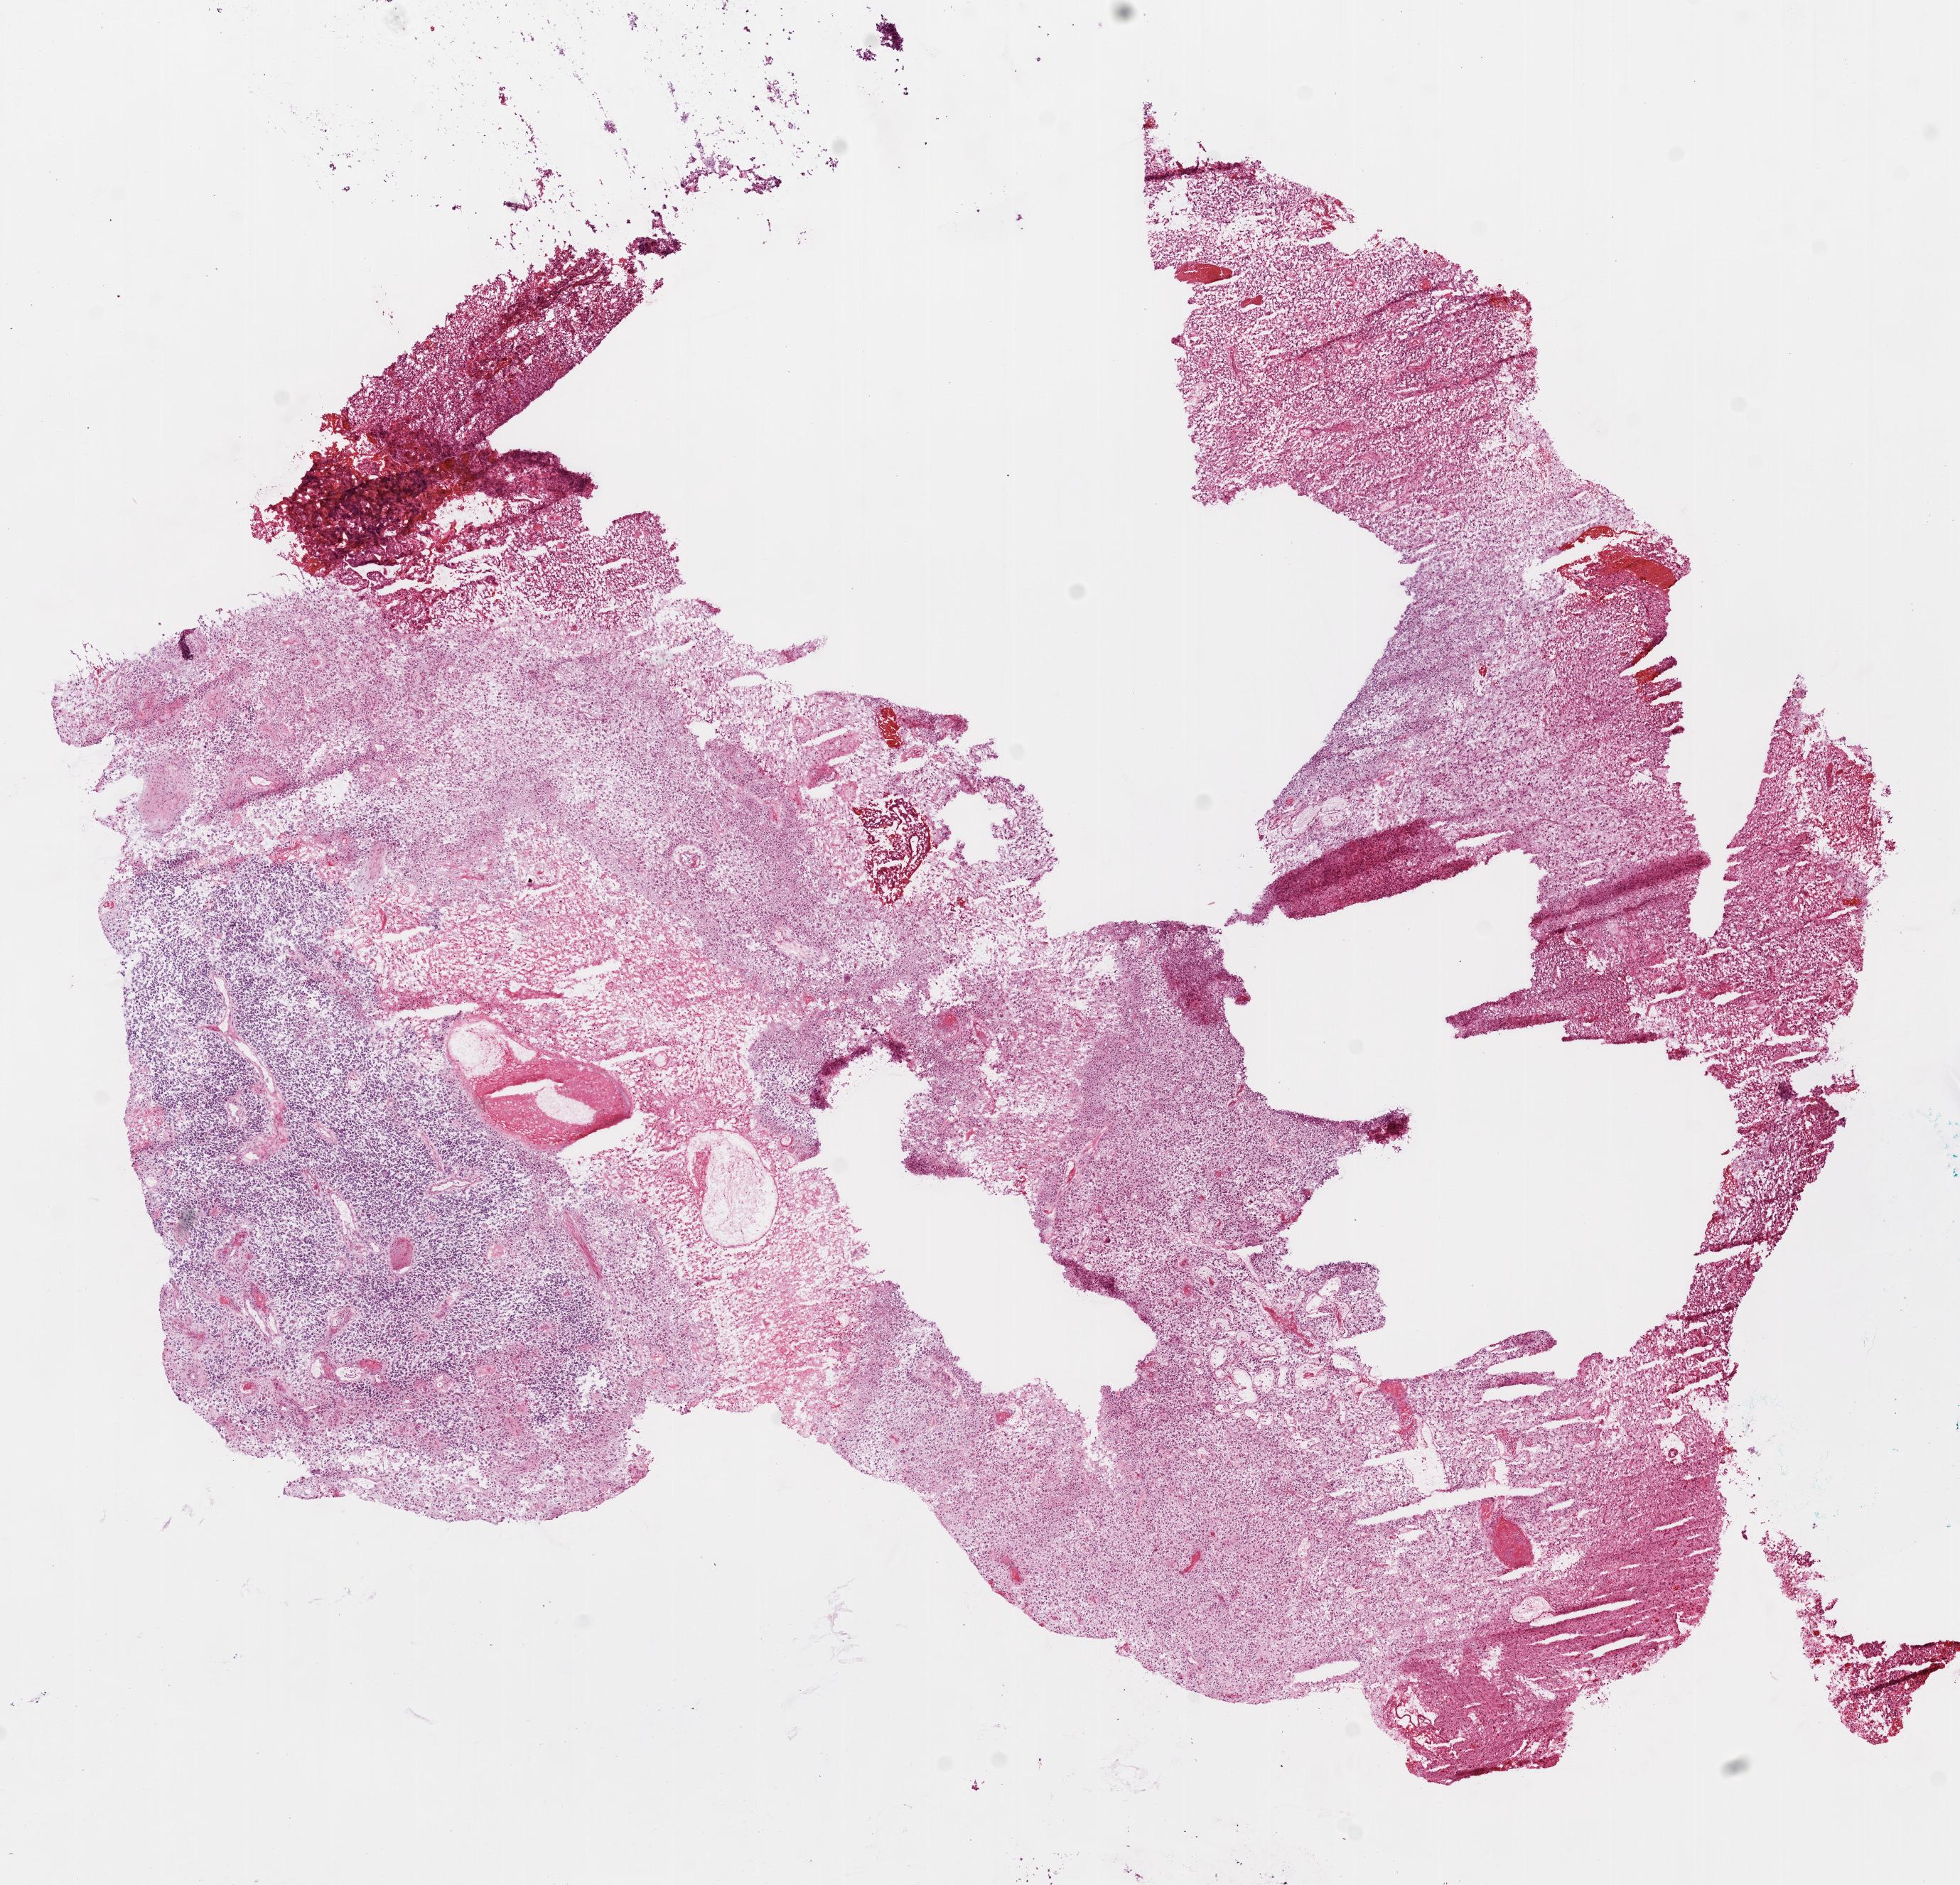
Digitized H&E tissue section (whole slide), shown as a low-resolution overview of the whole scanned area (about 11.1 x 10.7 mm, from a 20x scan), frozen section, primary tumour sample from the brain. Patient: male, age at initial diagnosis 46 years. Slide review estimates, as recorded: tumour cells 75%, tumour nuclei 100%, normal cells 0%, stromal cells 0%, necrosis 25%.
Histologic diagnosis: Glioblastoma.